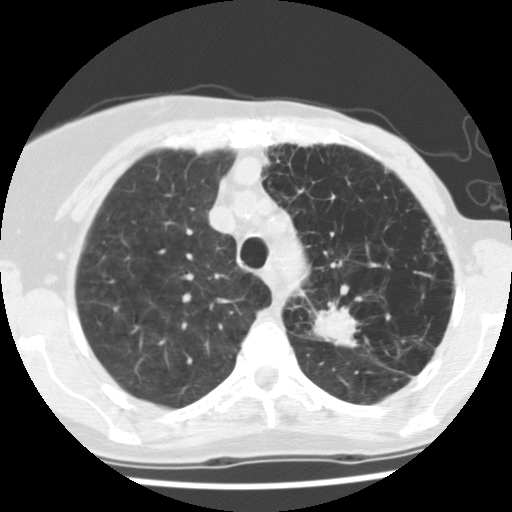
Axial slice from a low-dose chest CT screening exam. First (baseline) screen. Lung window (W 1500 / L -600 HU). 140 kVp. Slice 31 of 128 in the series. Female participant, aged 67 years at enrolment. Current smoker at enrolment.
Lesion marked by an expert reader, box from (x=299, y=286) to (x=382, y=362) px. The screening reader recorded 2 non-calcified nodules or masses ≥4 mm on this exam (left upper lobe, left lower lobe); which of them this box marks is not recorded. Official screen result: positive, change unspecified: nodule(s) >= 4 mm or enlarging nodule(s), mass(es), or other non-specific abnormalities suspicious for lung cancer. Participant outcome: lung cancer diagnosed 109 days after this screen — adenocarcinoma, NOS, left upper lobe, poorly differentiated (G3), stage IIB (AJCC 6th edition), 45 mm at pathology.